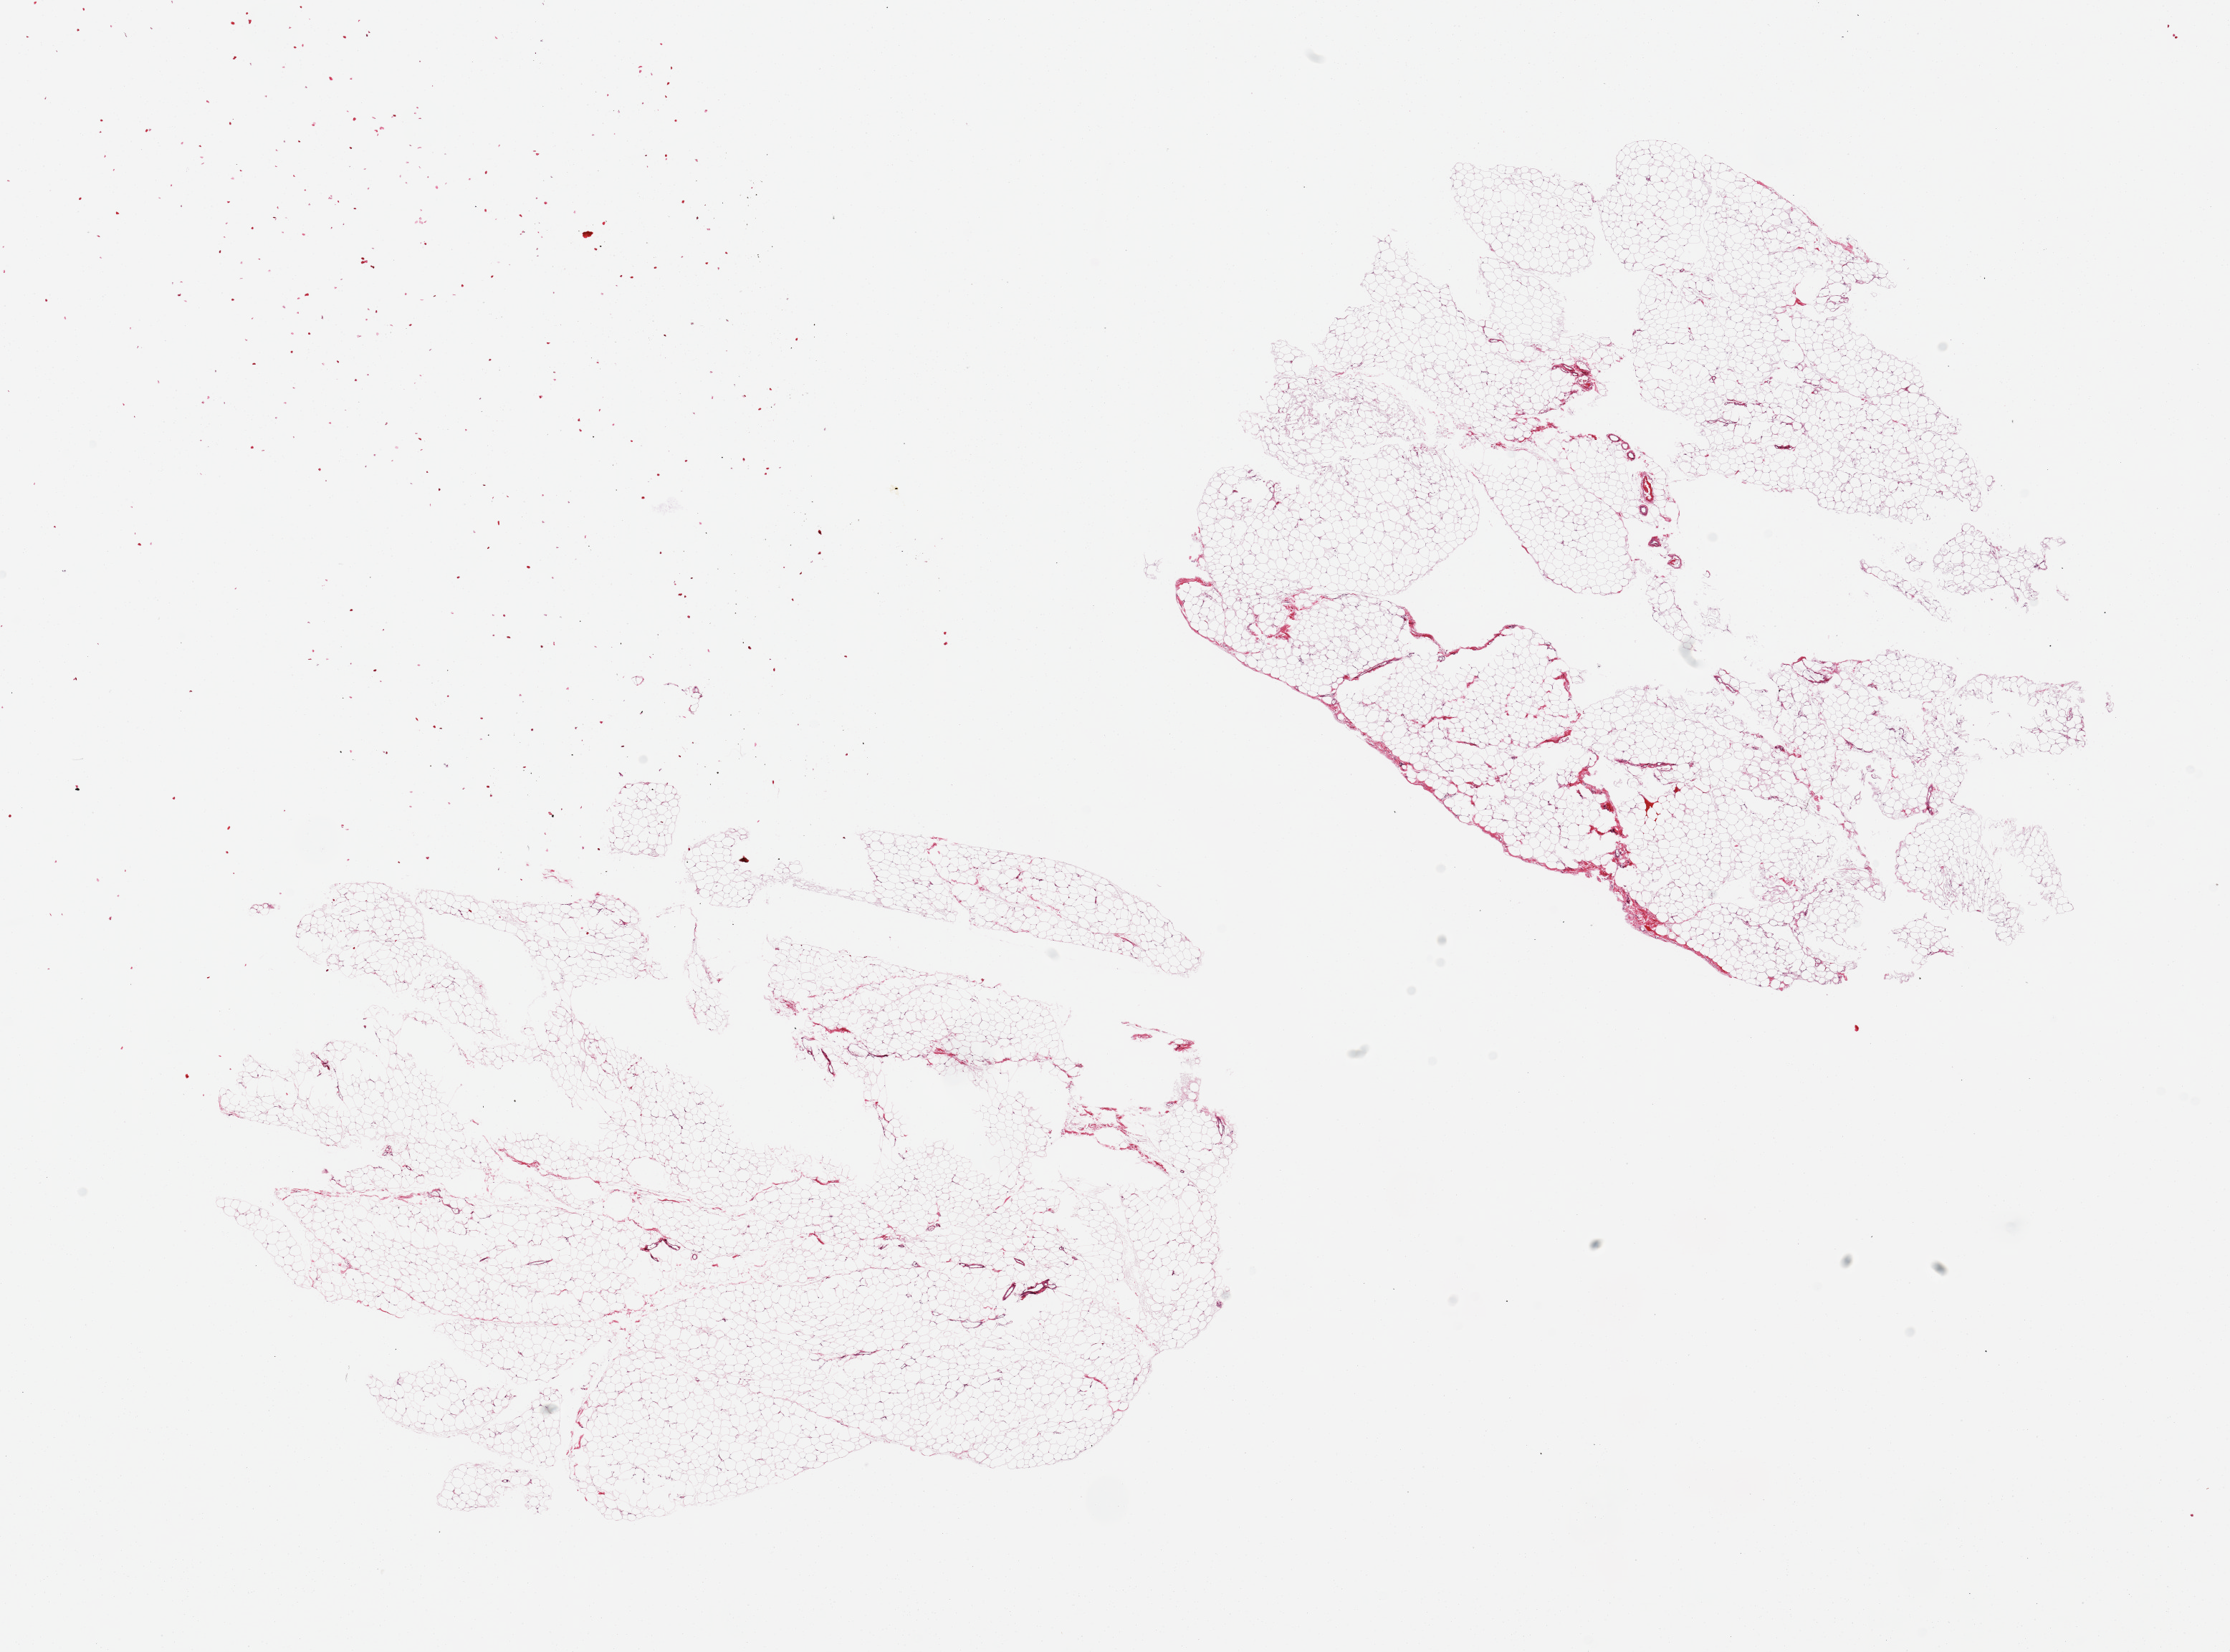
Whole-slide image, H&E stain, low-resolution overview of the scanned area, about 24.6 x 18.2 mm (slide scanned at 20x); PAXgene-fixed paraffin-embedded (PFPE) section; target tissue: omentum; donor tissue sample. Donor: female.
- review note (as recorded): 2 pieces, minimal fibrovascular tissue